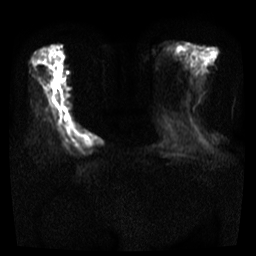
Breast MRI, one axial slice. Slice 9 of 35 in the series (ordered by position). Diffusion-weighted series; image 2 of 4 stored at this slice position (different b-values; order by instance number). 3 T. 5 mm slice thickness. 256 × 256 image matrix, field of view 300 × 300 mm. Female patient.
Annotated regions visible in this slice (manually delineated by an expert):
- tumour on diffusion-weighted imaging: box from (x=80, y=131) to (x=103, y=146) px